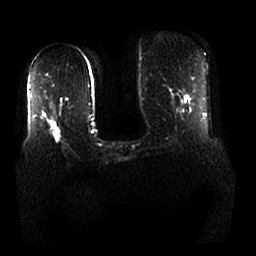
Breast MRI, one axial slice. Slice 13 of 25 in the series (ordered by position). Diffusion-weighted series; image 2 of 4 stored at this slice position (different b-values; order by instance number). 1.5 T. 4 mm slice thickness. 256 × 256 image matrix, field of view 380 × 380 mm. Female patient.
Annotated regions visible in this slice (manually delineated by an expert):
- tumour on diffusion-weighted imaging: bounding box [x1, y1, x2, y2] px = [57, 132, 62, 143]